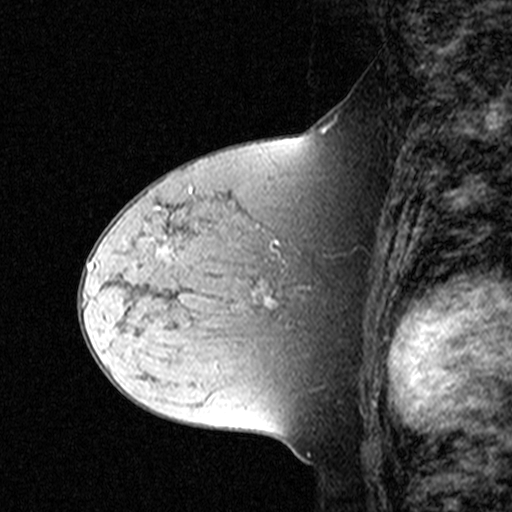
Breast MRI (dynamic contrast-enhanced), one sagittal slice. Slice 22 of 44 in the series (ordered by position). Dynamic contrast-enhanced study with each time point stored as its own series, time point 2 of 3 at this slice position (early post-contrast, ordered by acquisition time). 1.5 T. TE 4.5 ms, TR 11 ms. 512 × 512 image matrix, field of view 200 × 200 mm. Patient: female, 44 years. From the clinical record (not read from this slice): setting: breast cancer imaged before/during neoadjuvant chemotherapy; receptor status: triple-negative.
Annotated regions visible in this slice (semi-automatically segmented with operator editing):
- analysis volume of interest (the breast-tissue region the enhancement analysis was run in; not a lesion): bounding box <132,212,309,331> (left, top, right, bottom; pixels)
- tumour enhancement mask (voxels above the 90 % enhancement threshold inside the analysis volume of interest): <161,247,269,302>